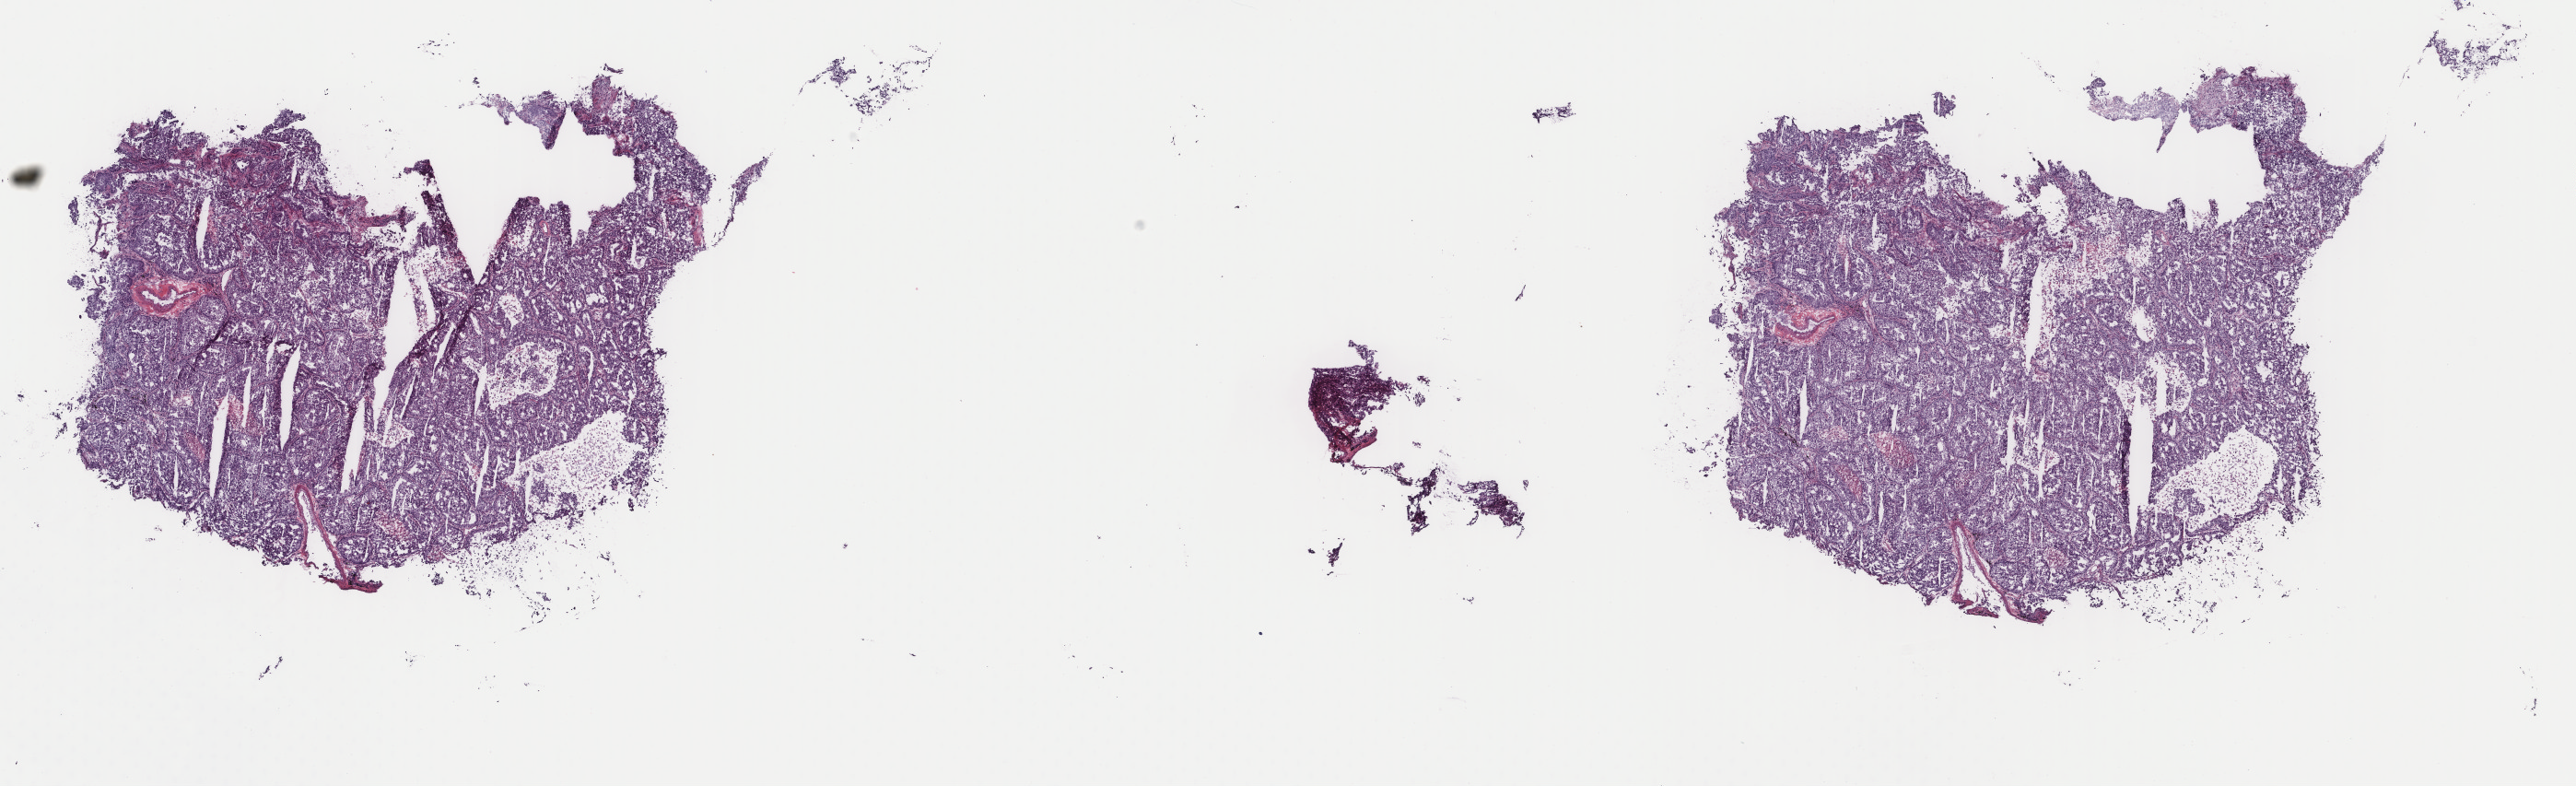
Hematoxylin and eosin (H&E) stained whole-slide image, a low-resolution overview of the entire scanned area, about 22.2 x 6.8 mm (acquisition: 40x scan), frozen section from the top of the tissue portion, lung, primary tumour sample. Male patient; age at initial diagnosis 84 years. Pathologist review of this section (percent, as recorded): tumour cells 95%, tumour nuclei 80%, normal cells 0%, stromal cells 0%, necrosis 5%. Inflammatory infiltration, as recorded: lymphocyte infiltration 2%, monocyte infiltration 4%, neutrophil infiltration 0%.
Diagnosis: Acinar cell carcinoma (upper lobe, lung). AJCC pathologic stage: IB (6th edition).